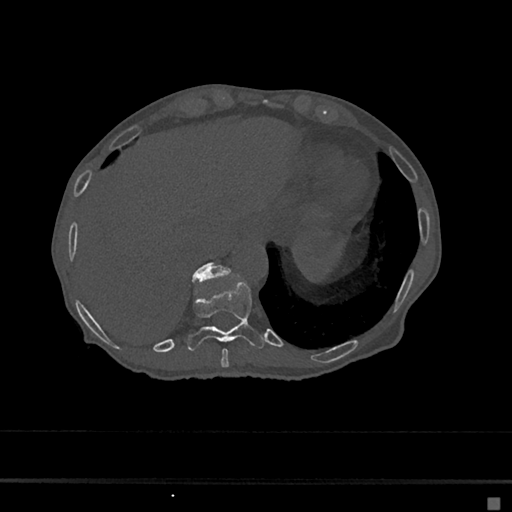
CT including the spine, one axial slice. Slice 224 of 797 in the series (ordered by position). 120 kVp. Bone window (W 1800 / L 400 HU). 512 × 512 image matrix. Patient: female, 68 years. Case-level facts recorded for this patient, not image findings: primary cancer: renal.
Structures marked on this image (semi-automatically segmented with operator editing):
- T10 vertebra: bounding box [x1, y1, x2, y2] px = [187, 281, 264, 351]
- T11 vertebra: [192, 262, 229, 283]
- T9 vertebra: [221, 348, 229, 367]